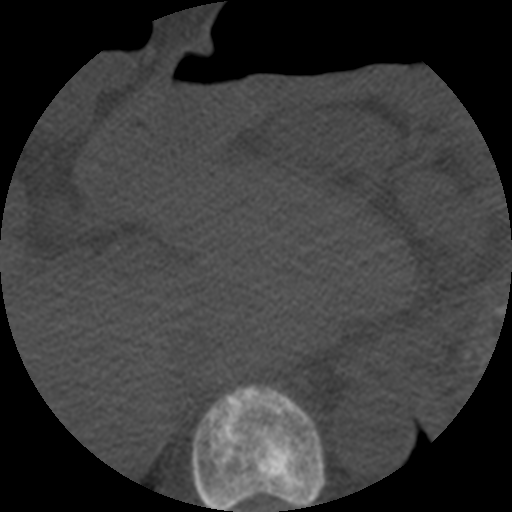
CT including the spine, one axial slice. Slice 261 of 508 in the series (ordered by position). Reconstruction kernel STANDARD. Bone window (W 1800 / L 400 HU). 1.25 mm slice thickness. 512 × 512 image matrix, field of view 160 × 160 mm. Patient age 57 years. Case-level facts recorded for this patient, not image findings: primary cancer: prostate.
Outlined on this slice (semi-automatic segmentation, software-assisted and operator-edited):
- T10 vertebra: bounding box (x1, y1, x2, y2) in pixels: (191, 384, 325, 512)